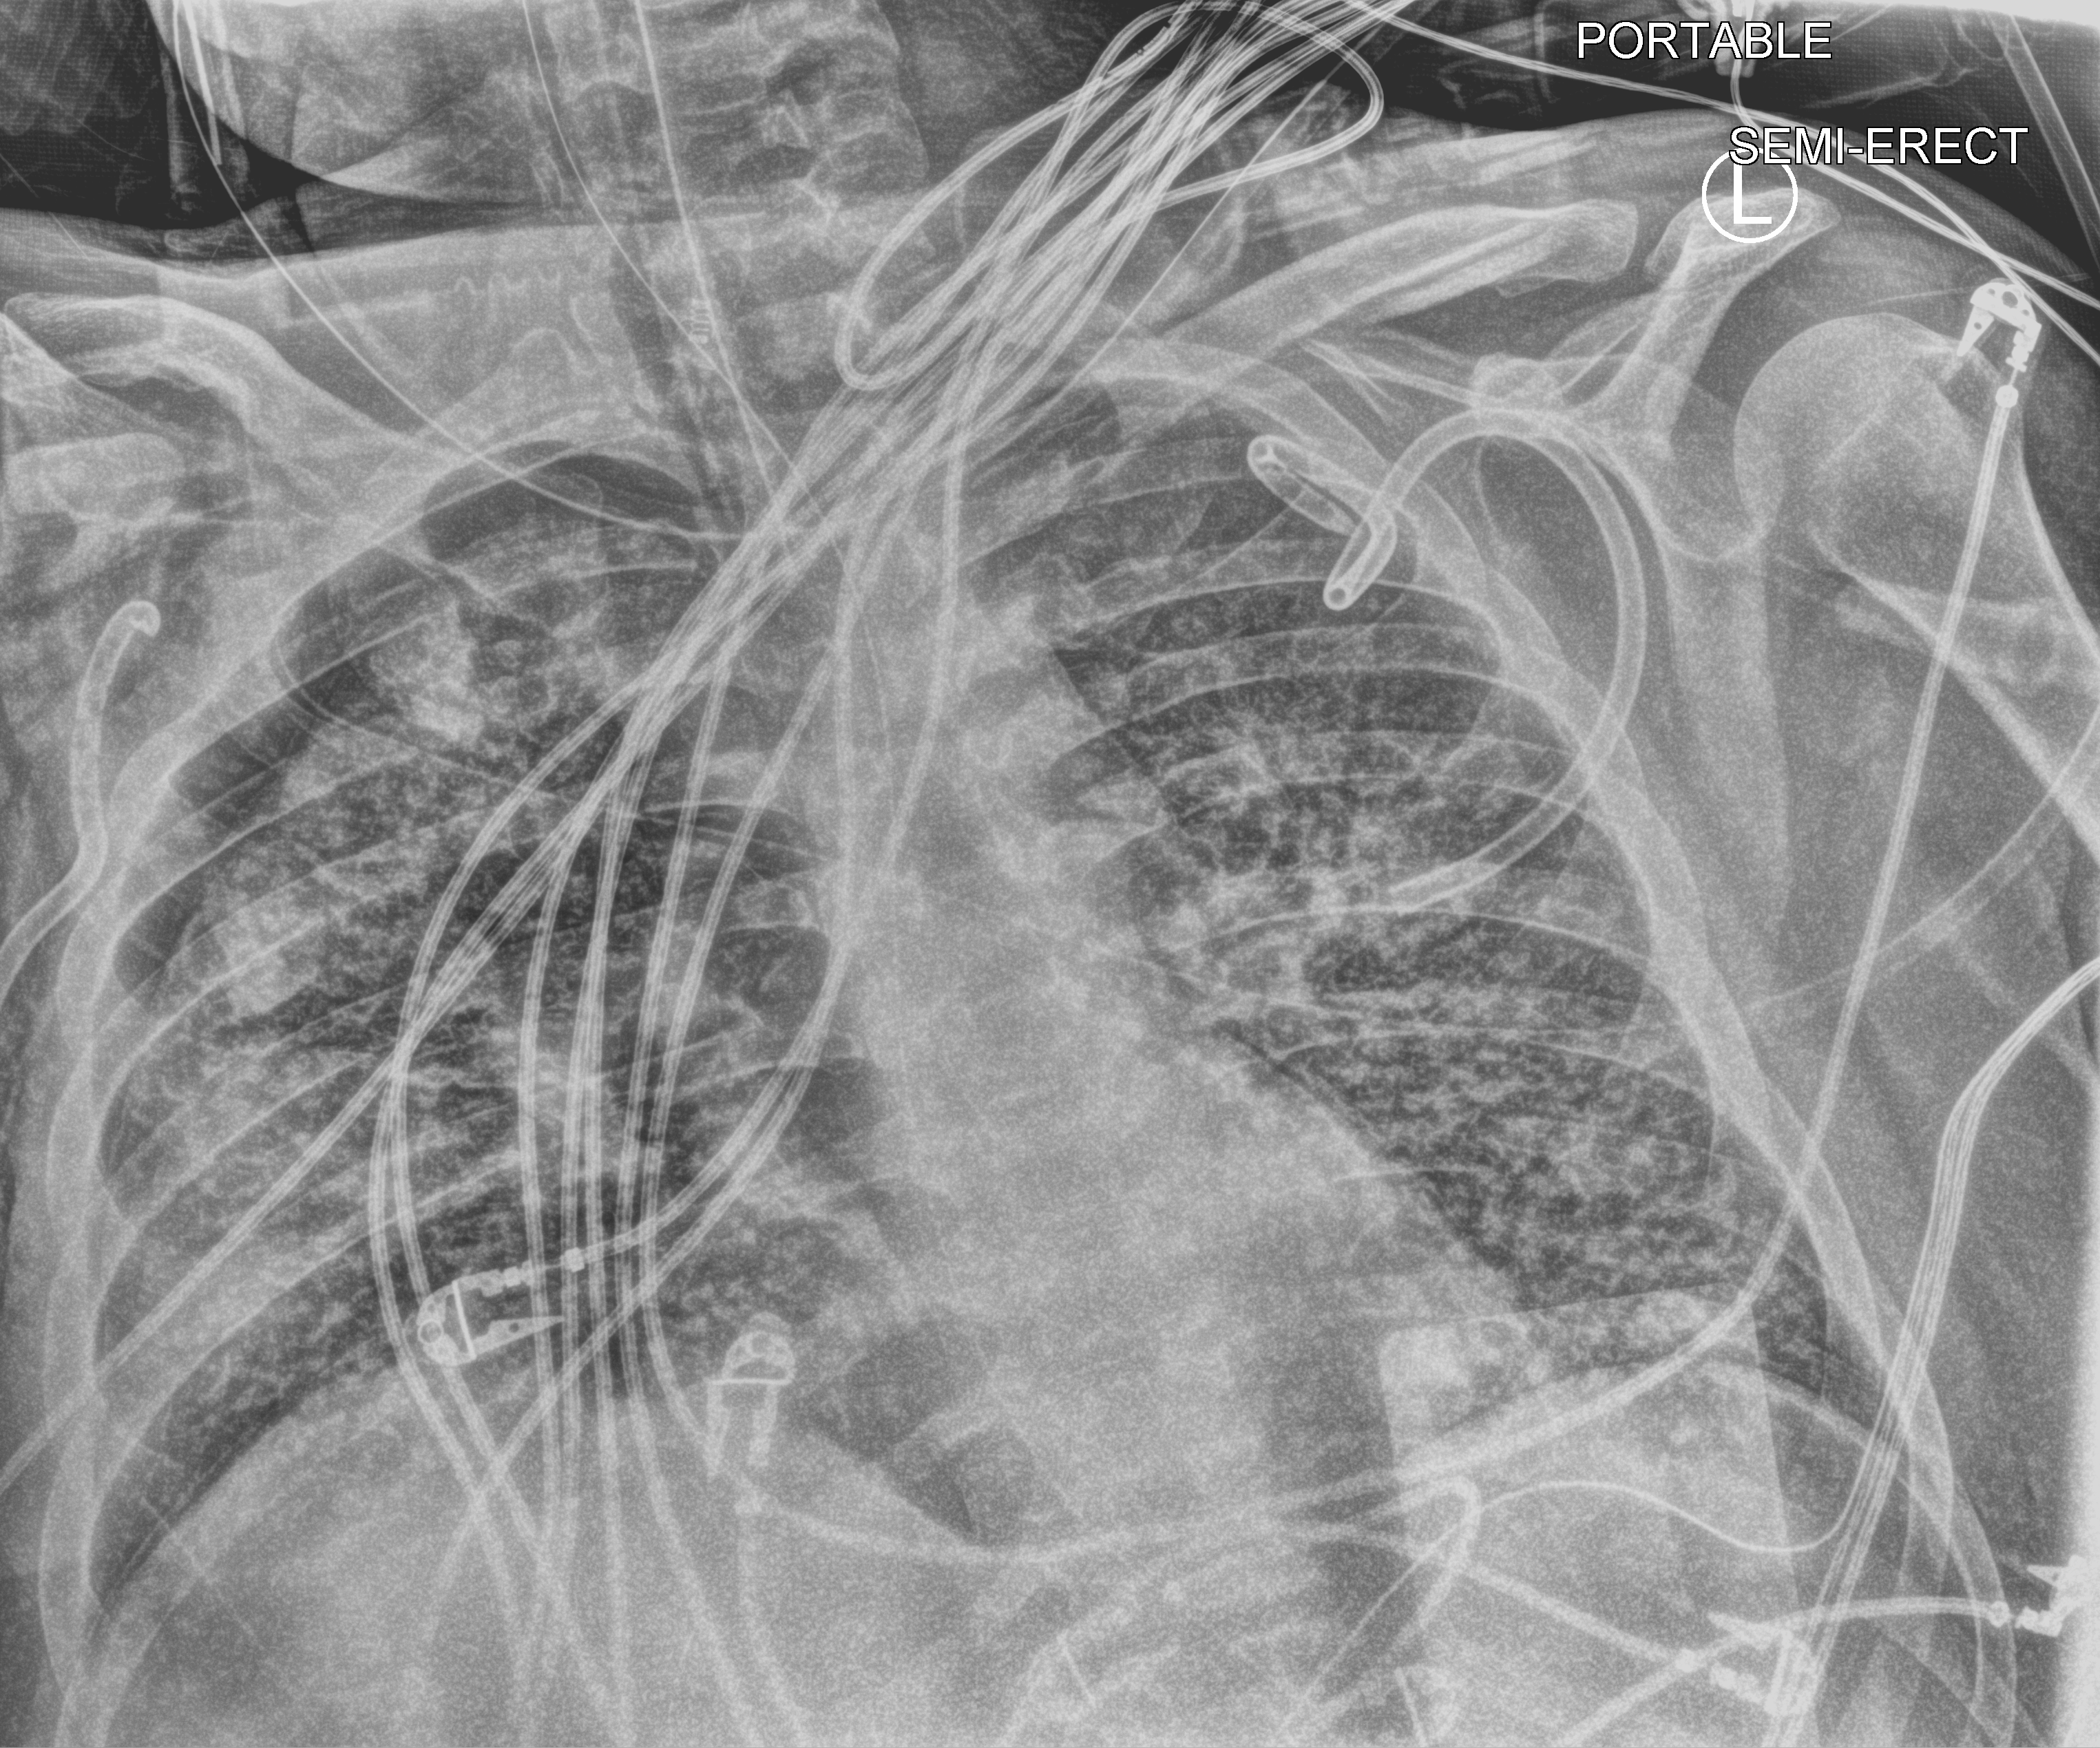
Chest X-ray (portable), anteroposterior (AP) projection. Adult patient hospitalised with COVID-19, age 18–59 years.
Admission-level facts for this patient (not findings on this image; timing relative to this image not recorded): admitted to intensive care during this hospital stay: yes; mechanically ventilated during this hospital stay: yes.